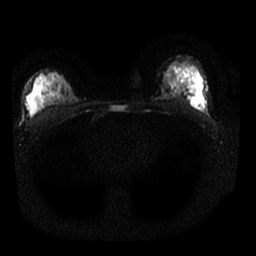
Breast MRI, one axial slice; position 16 of 25 along the scan axis; diffusion-weighted series; image 2 of 4 stored at this slice position (different b-values; order by instance number); 1.5 T; 4 mm slice thickness; 256 × 256 image matrix, field of view 320 × 320 mm. Female patient.
Outlined on this slice (manually delineated by an expert):
- tumour on diffusion-weighted imaging: bounding box <191,100,198,106> (left, top, right, bottom; pixels)